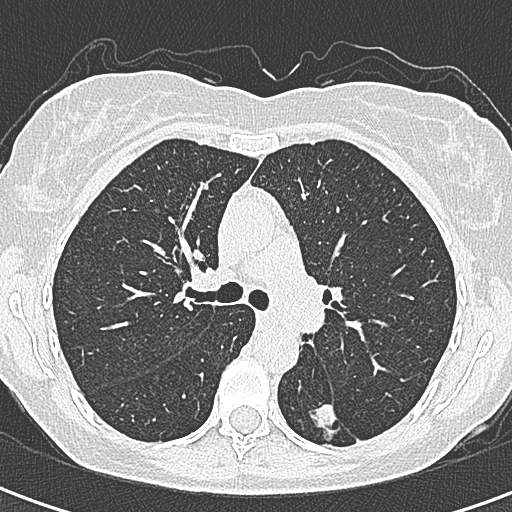
Axial slice from a low-dose chest CT screening exam, first (baseline) screen, lung window (W 1500 / L -600 HU), 1 mm slice thickness, lung (sharp) reconstruction kernel (B80f), 120 kVp, 512 × 512 image matrix, field of view 284 × 284 mm. Female, age 58 years at enrolment. Former smoker at enrolment.
Lesion marked by an expert reader, bounding box [x1, y1, x2, y2] px = [290, 391, 361, 454]. The screening reader recorded 2 non-calcified nodules or masses ≥4 mm on this exam (left lower lobe, right lower lobe); which of them this box marks is not recorded. Lung cancer was diagnosed 22 days after this screen: adenocarcinoma, NOS, left lower lobe, moderately differentiated (G2), stage IA (AJCC 6th edition), 25 mm at pathology.